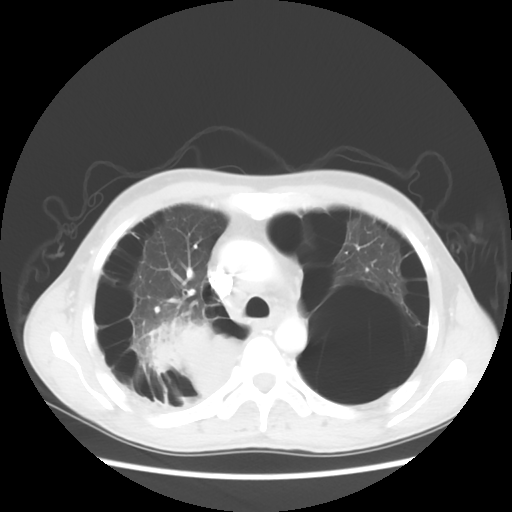
Chest CT, one axial slice; position 38 of 56 along the scan axis; reconstruction kernel STANDARD; lung window (W 1500 / L -600 HU); 5 mm slice thickness; 512 × 512 image matrix, field of view 351 × 351 mm. Patient: male, 41 years. Case-level facts recorded for this patient, not image findings: clinical TNM (as recorded): T4 N0 M1a; histopathological grade: G3.
Structures marked on this image (bounding box drawn by a radiologist):
- lung tumour (recorded histology: large cell carcinoma): bounding box (x1, y1, x2, y2) in pixels: (148, 318, 234, 398)